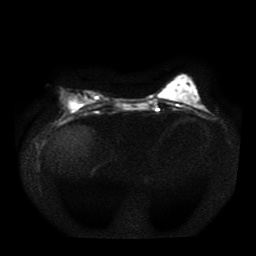
Breast MRI, one axial slice. Slice 16 of 41 in the series (ordered by position). Diffusion-weighted series; image 2 of 4 stored at this slice position (different b-values; order by instance number). 1.5 T. 5 mm slice thickness. 256 × 256 image matrix, field of view 330 × 330 mm. Female patient.
Annotated regions visible in this slice (outlined manually by an expert reader):
- tumour on diffusion-weighted imaging: box from (x=70, y=103) to (x=78, y=109) px